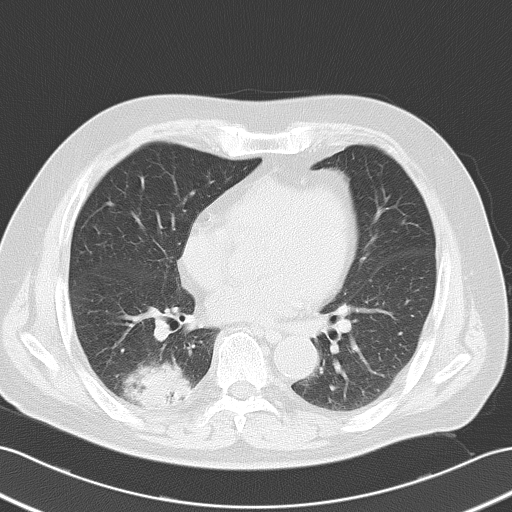
Chest CT, one axial slice; position 18 of 52 along the scan axis; reconstruction kernel B70f; 120 kVp; lung window (W 1500 / L -600 HU); 5 mm slice thickness; 512 × 512 image matrix. Patient: male, 70 years. From the clinical record (not read from this slice): clinical TNM (as recorded): T2 N0 M0; histopathological grade: G2.
Structures marked on this image (bounding box drawn by a radiologist):
- lung tumour (recorded histology: adenocarcinoma): bounding box (x1, y1, x2, y2) in pixels: (119, 361, 195, 407)